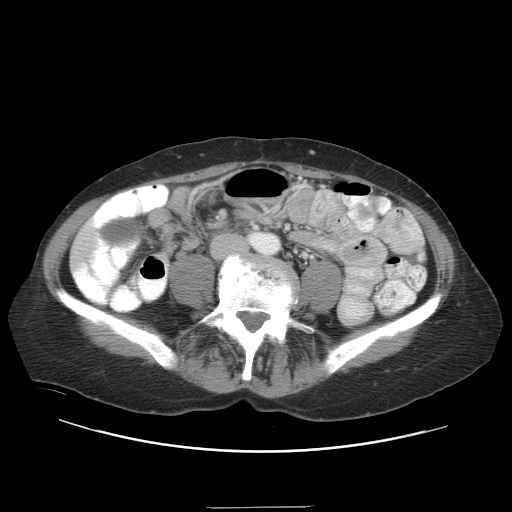
Contrast-enhanced abdominal CT, one axial slice; slice 1 of 38 in the series (ordered by position); reconstruction kernel STANDARD; 120 kVp; soft-tissue window (W 400 / L 40 HU); 5 mm slice thickness; 512 × 512 image matrix, field of view 388 × 388 mm. Female patient, age 64 years. From the clinical record (not read from this slice): diagnosis: colorectal cancer liver metastases, imaged before liver resection; multiple liver metastases: no; largest metastasis: 3.8 cm; disease in both lobes: yes.
Outlined on this slice (manually delineated by an expert):
- liver: bounding box [x1, y1, x2, y2] px = [72, 225, 95, 267]